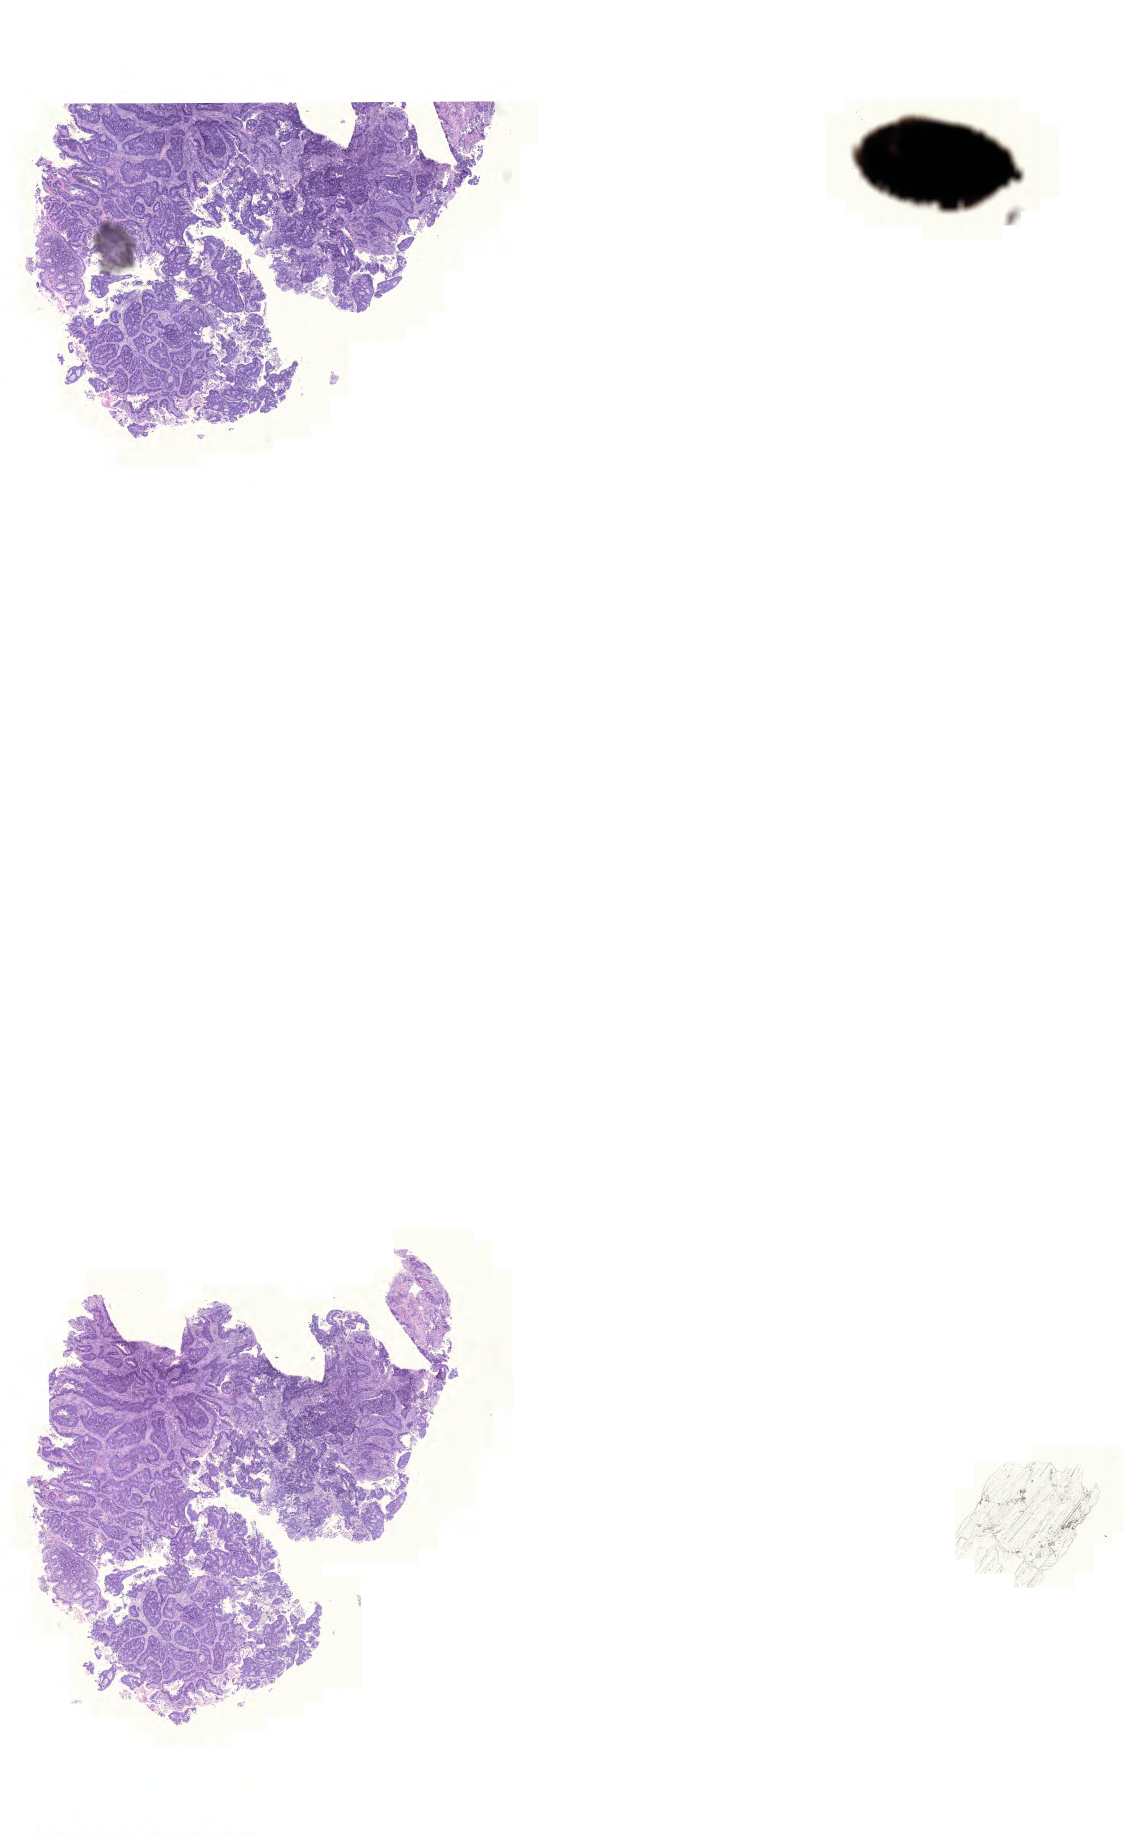
Hematoxylin and eosin (H&E) stained whole-slide image, shown as a low-resolution overview of the whole scanned area (about 16.7 x 27.3 mm, acquisition: 20x scan), formalin-fixed paraffin-embedded (FFPE) diagnostic section, rectum, primary tumour sample. Patient: male, age at initial diagnosis 69 years.
Lymph nodes positive (case pathology): 0 of 15 examined. AJCC pathologic stage: I. Diagnosis: Adenocarcinoma, NOS.